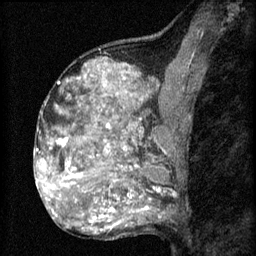
Breast MRI (dynamic contrast-enhanced), one sagittal slice; position 35 of 60 along the scan axis; 3 images stored at this slice position (order not interpretable as contrast timing); 1.5 T; TE 4.2 ms, TR 8.2 ms; 2 mm slice thickness; 256 × 256 image matrix, field of view 180 × 180 mm. Female patient, age 48 years.
Structures marked on this image (semi-automatic segmentation, software-assisted and operator-edited):
- analysis volume of interest (the breast-tissue region the enhancement analysis was run in; not a lesion): bounding box [x1, y1, x2, y2] px = [61, 138, 153, 201]
- tumour enhancement mask (voxels above the 70 % enhancement threshold inside the analysis volume of interest): [61, 138, 141, 199]